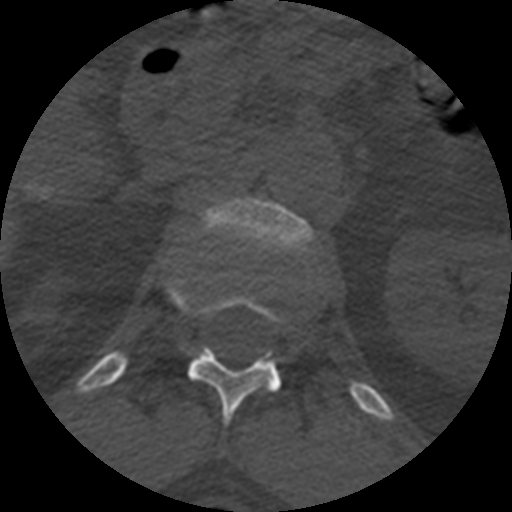
CT including the spine, one axial slice. Position 379 of 399 along the scan axis. Reconstruction kernel STANDARD. Bone window (W 1800 / L 400 HU). 1.25 mm slice thickness. 512 × 512 image matrix, field of view 160 × 160 mm. Patient age 71 years. Case-level facts recorded for this patient, not image findings: primary cancer: prostate.
Annotated regions visible in this slice (semi-automatic segmentation, software-assisted and operator-edited):
- L1 vertebra: bounding box <198,199,316,255> (left, top, right, bottom; pixels)
- T12 vertebra: <167,280,282,426>